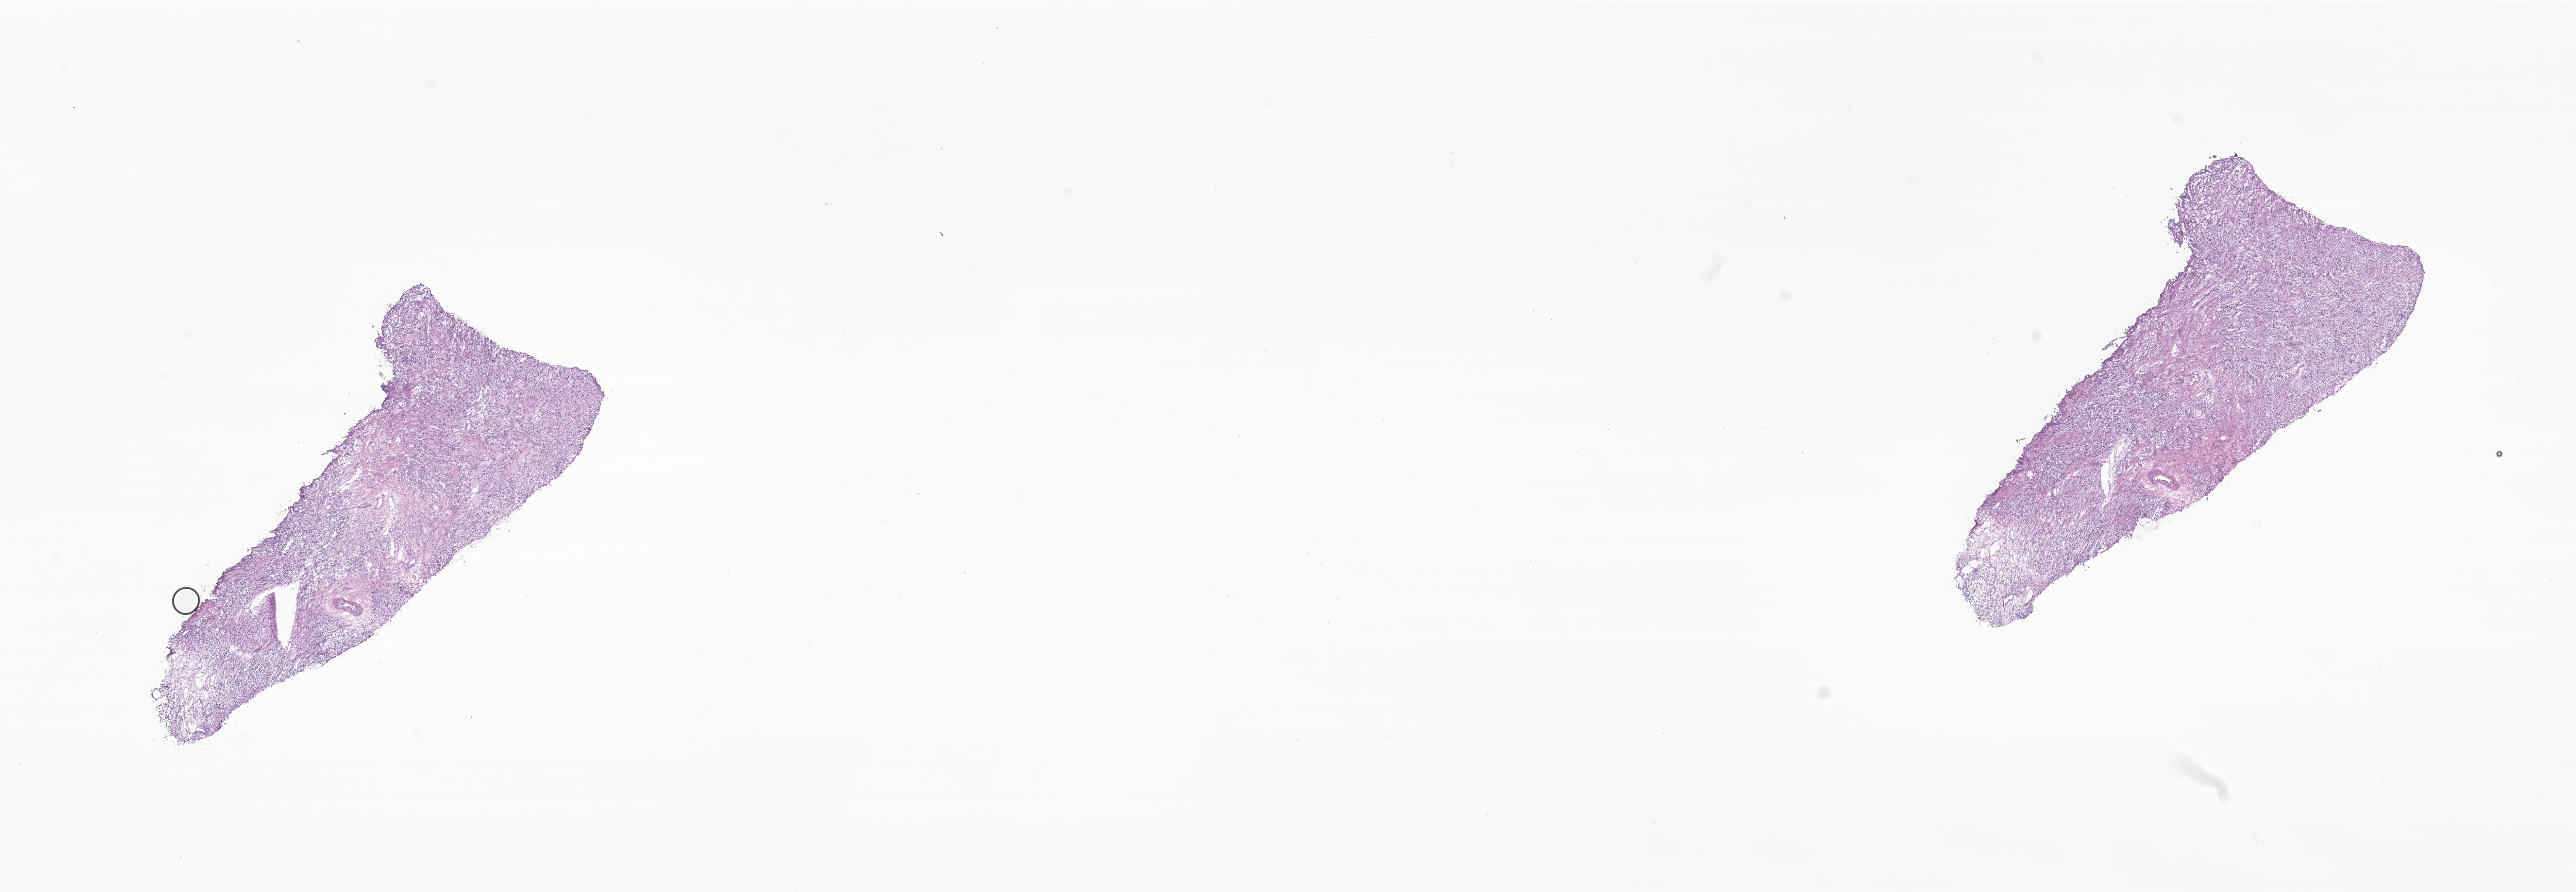
H&E whole-slide image of tumor tissue from the scrotum — shown as a low-resolution overview of the whole scanned area (about 31.9 x 11.1 mm); cryosection (OCT / tissue freezing medium). Patient male; age 213 months.
Diagnosis (ICD-O-3 morphology term): Embryonal rhabdomyosarcoma, NOS.